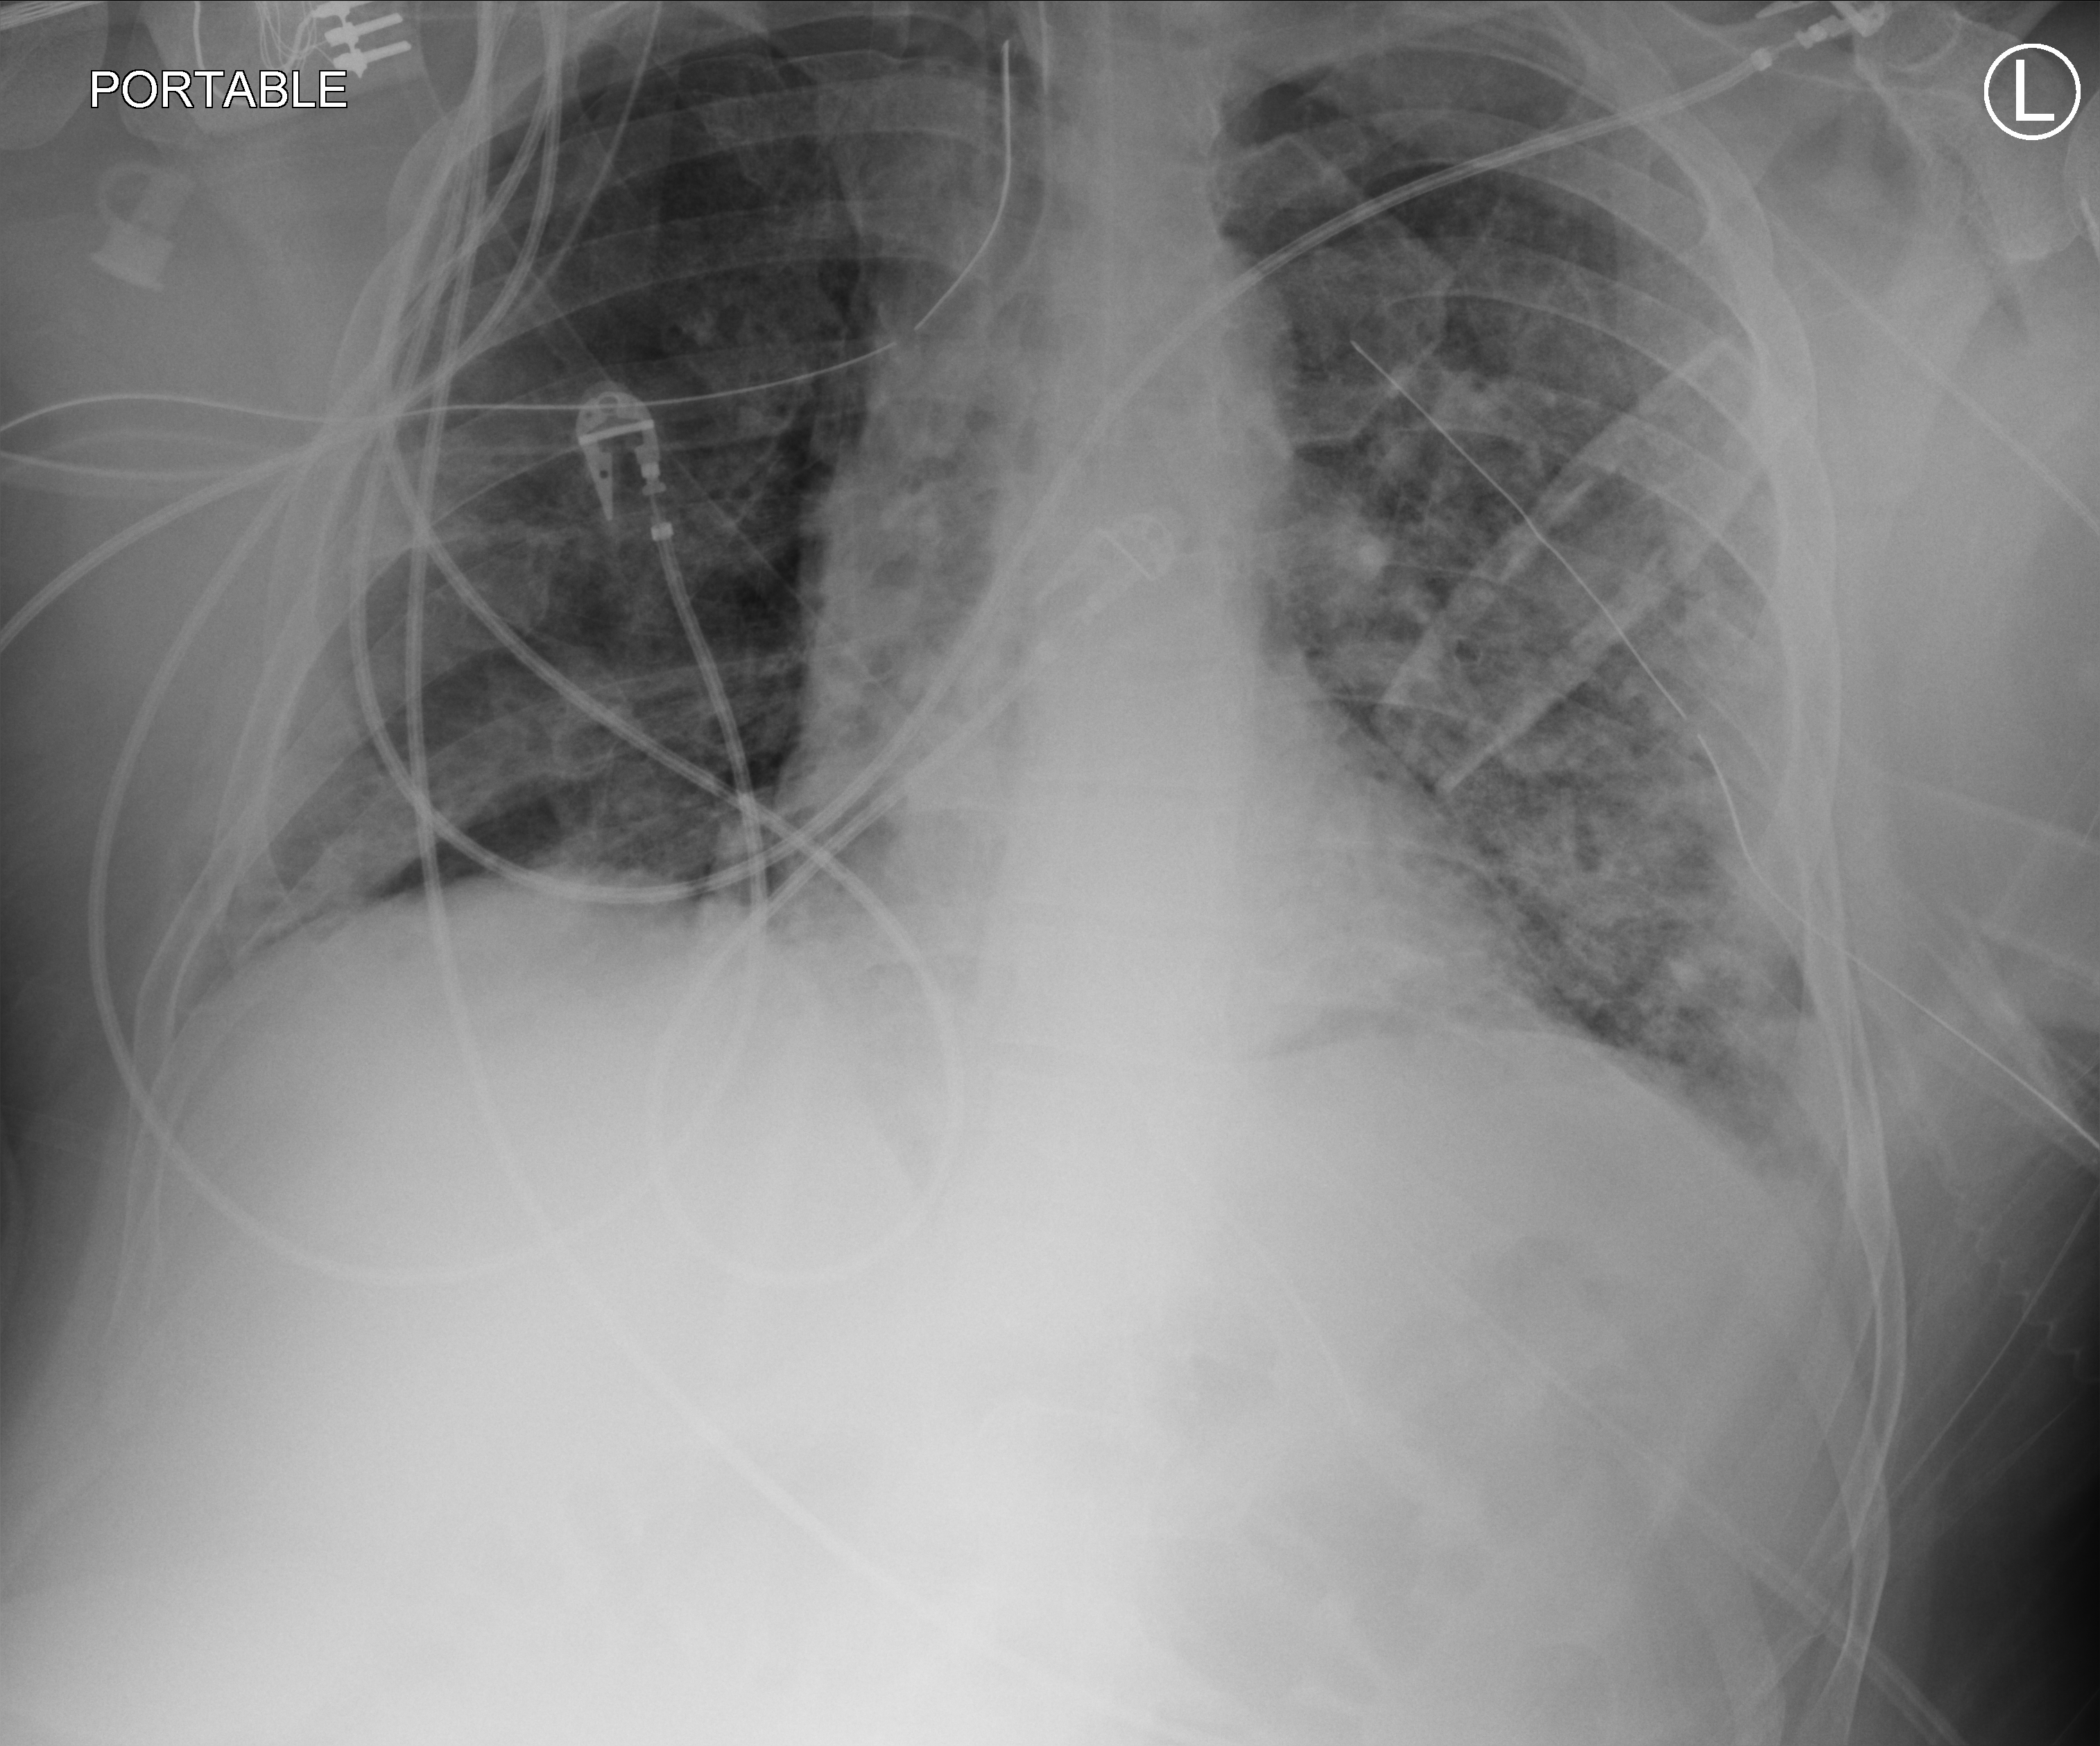
Portable chest radiograph, anteroposterior (AP) projection. Patient hospitalised with COVID-19; male, aged 18–59 years.
From the hospital-stay record, not from the radiograph (when in the stay this image was taken is not recorded): length of hospital stay: 63 days; mechanically ventilated during this hospital stay: yes; smoking status (admission record): never.